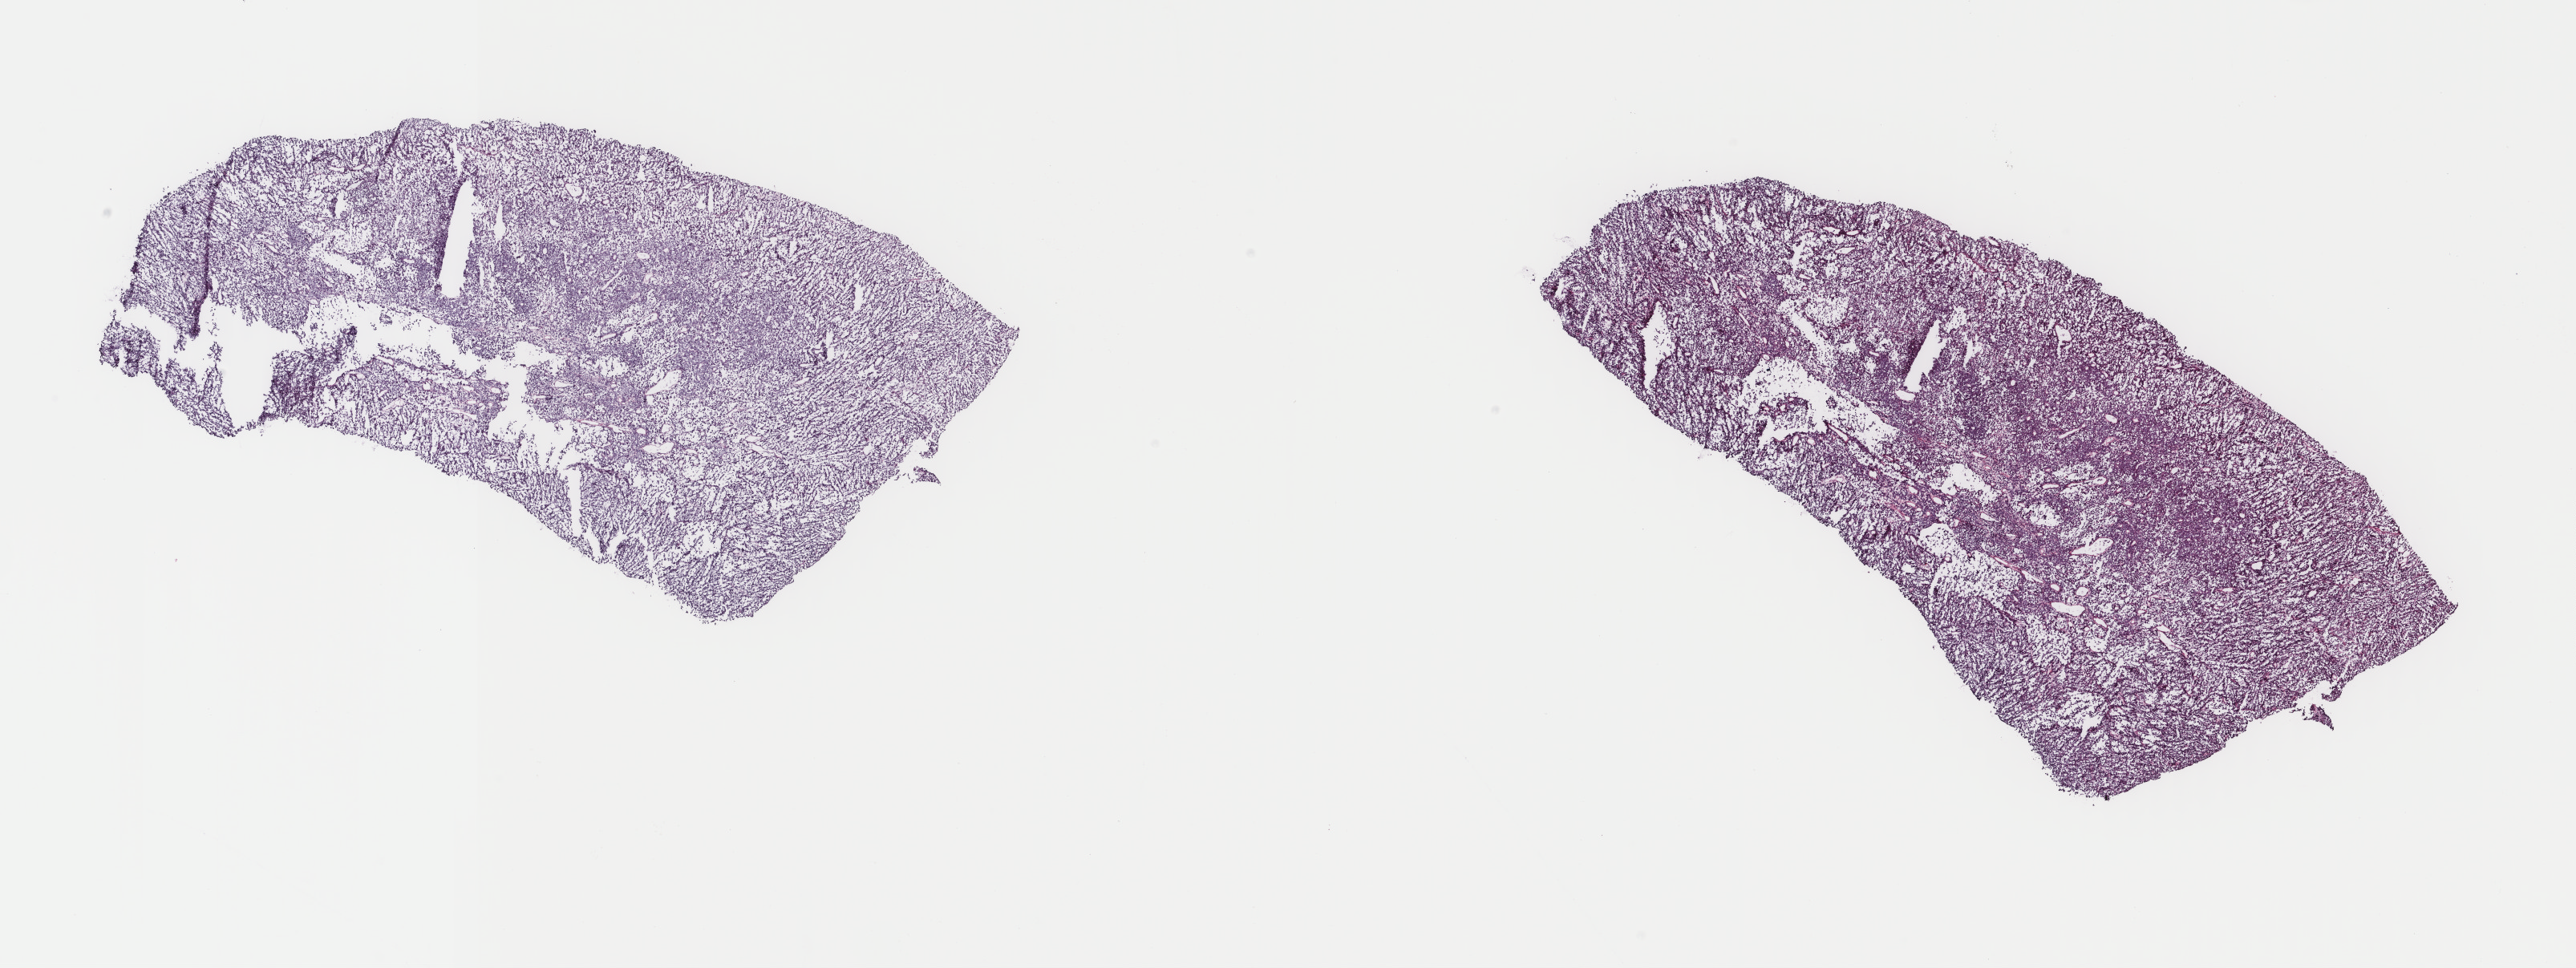
Whole-slide histology image, H&E-stained, a low-resolution overview of the entire scanned area, about 25.5 x 9.6 mm (acquisition: 40x scan); frozen section from the top of the tissue portion; metastatic tumour sample. Male patient; age at initial diagnosis 48 years. Pathologist review of this section (percent, as recorded): tumour cells 100%, tumour nuclei 95%, normal cells 0%, stromal cells 0%, necrosis 0%. Infiltration values recorded for this section: lymphocyte infiltration 2%, monocyte infiltration 0%, neutrophil infiltration 0%.
This section: metastatic tumour tissue. Patient diagnosis: Malignant melanoma, NOS.